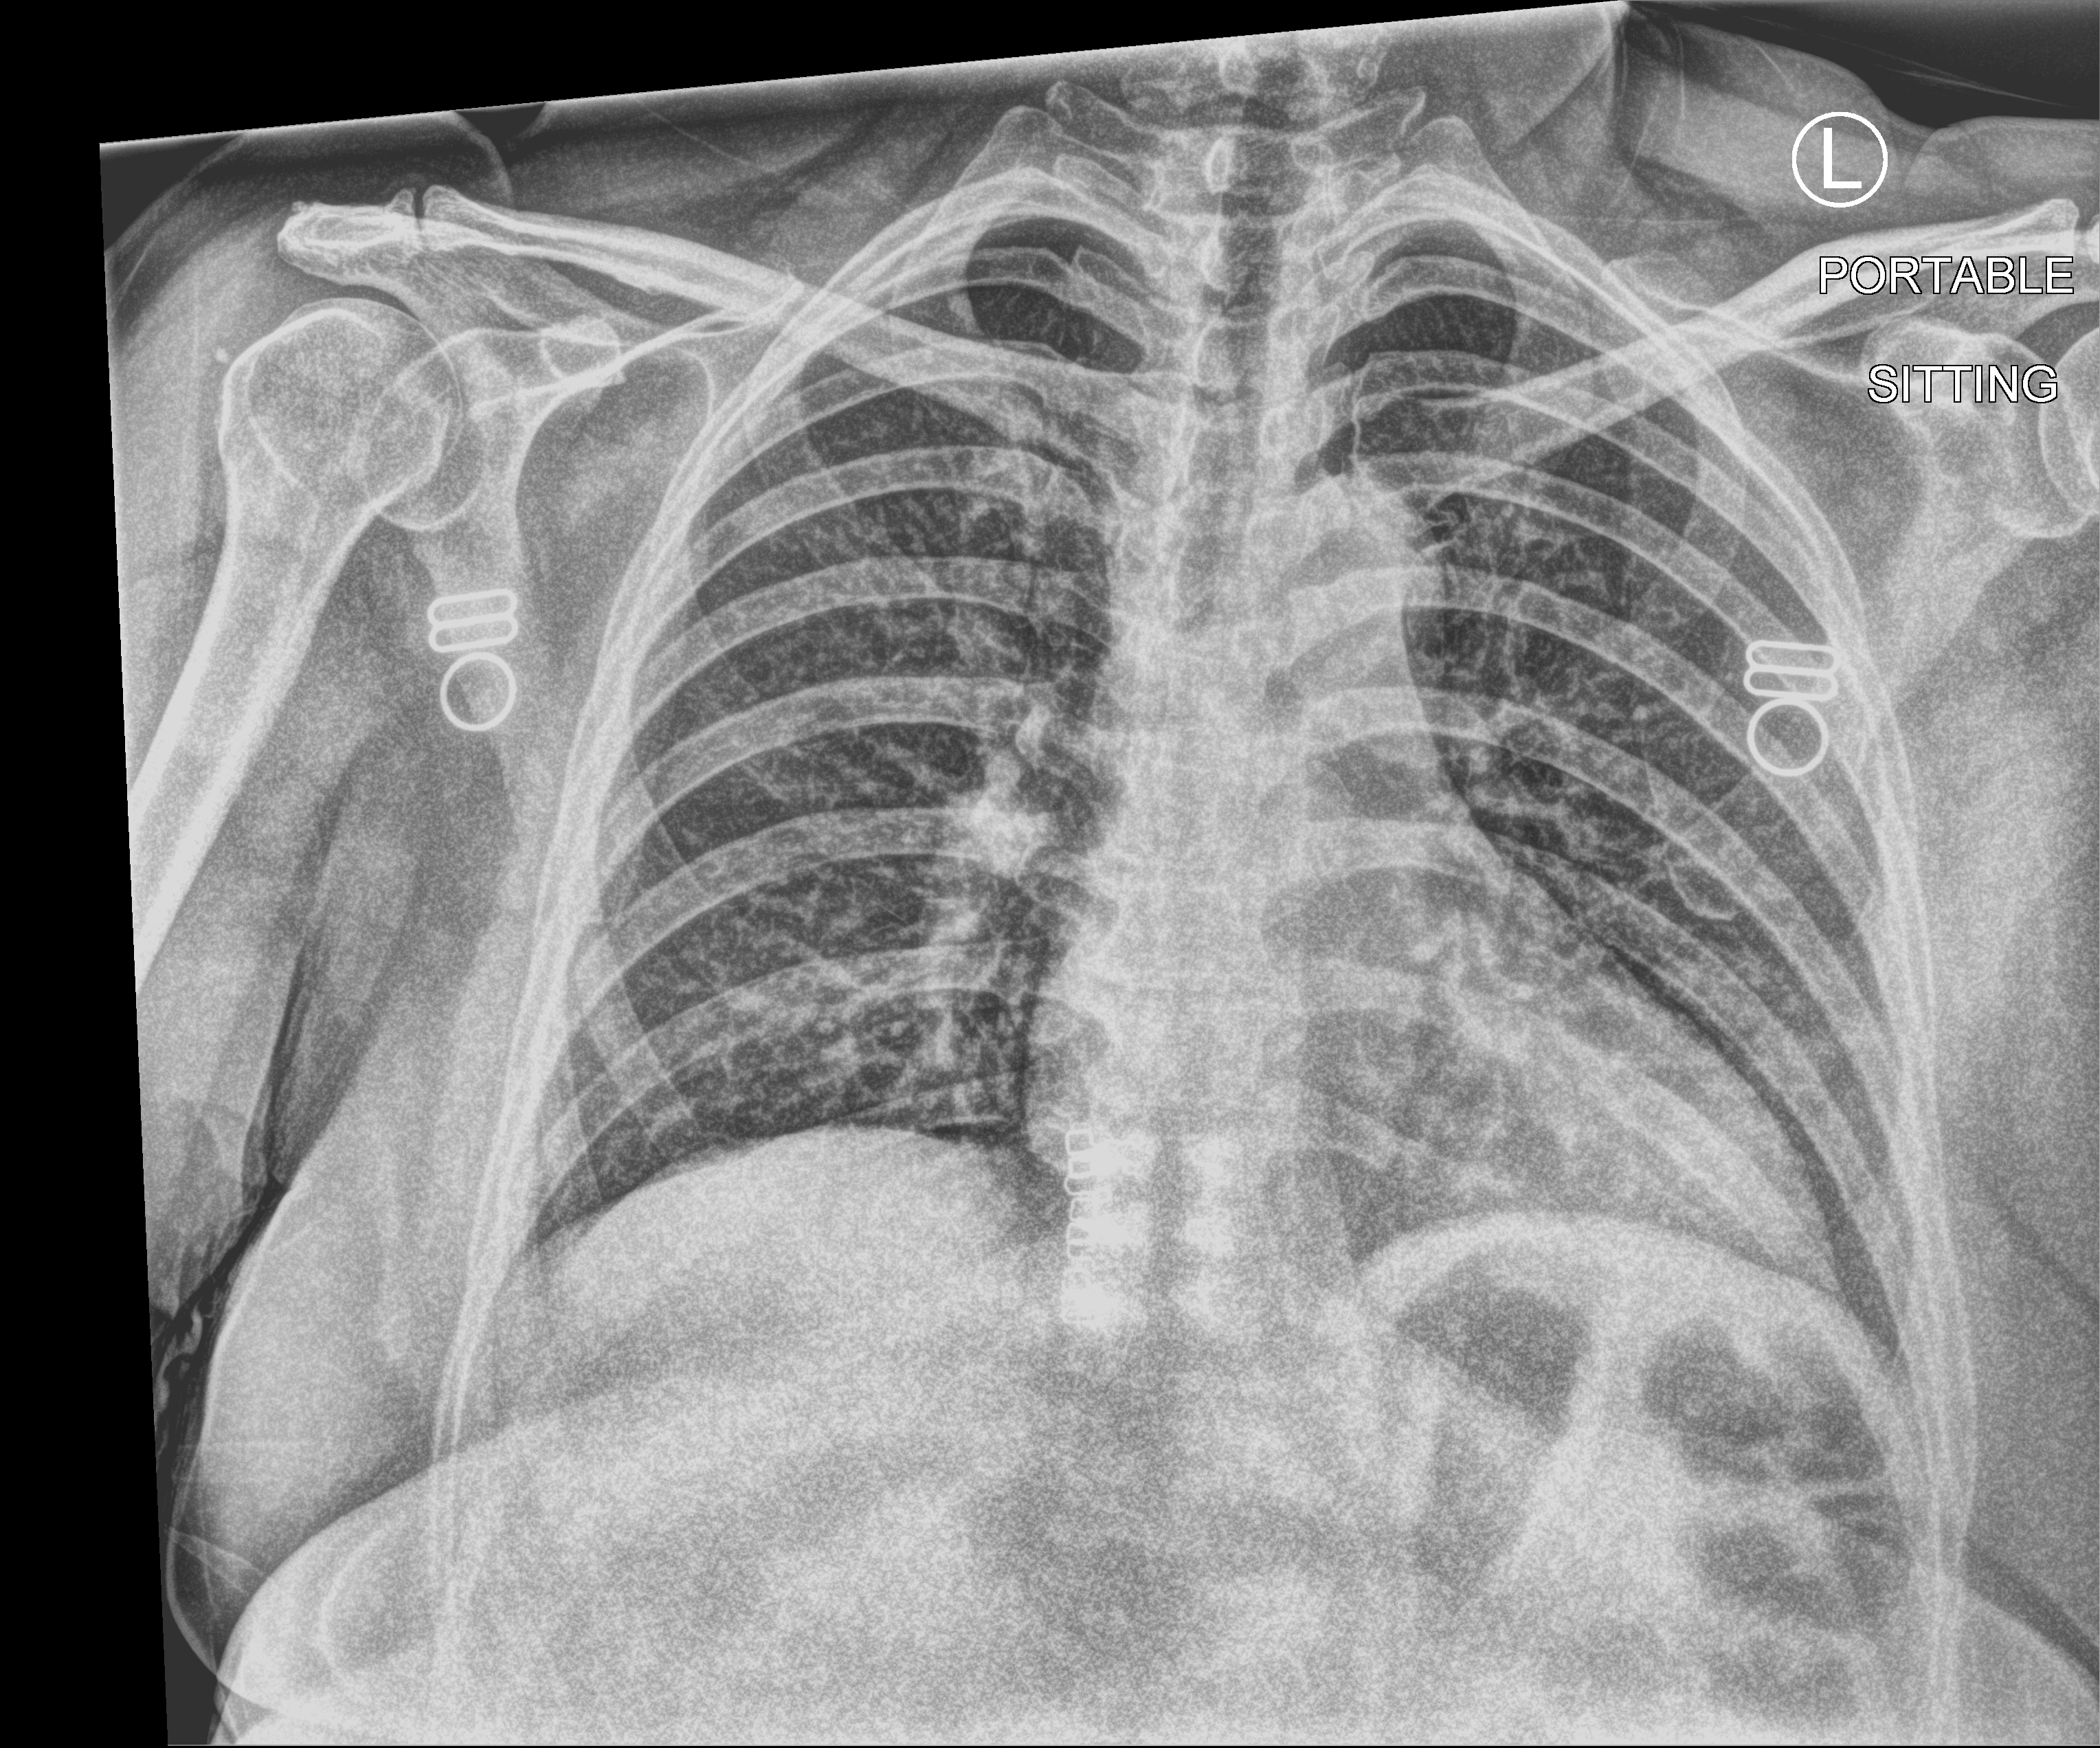
Chest X-ray (portable); anteroposterior (AP) projection. Female patient hospitalised with COVID-19, age 60–74 years.
Hospital-stay facts (about this admission, not read from this image; timing relative to this image not recorded):
- admitted to intensive care during this hospital stay: no